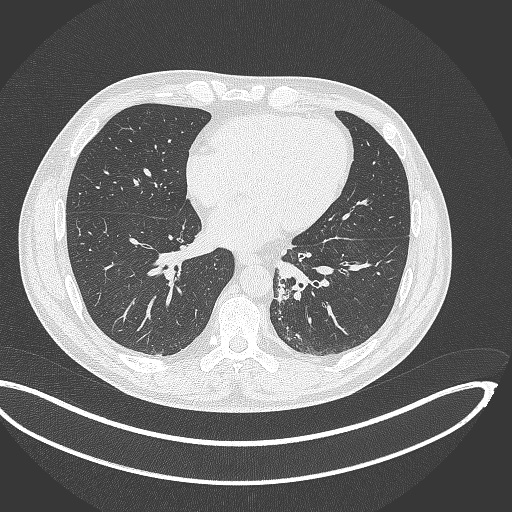
Chest CT, one axial slice; slice 137 of 362 in the series (ordered by position); reconstruction kernel B70f; 120 kVp; lung window (W 1500 / L -600 HU); 512 × 512 image matrix, field of view 442 × 442 mm. Male patient, age 50 years. From the clinical record (not read from this slice): clinical TNM (as recorded): T2a N3 M0.
Annotated regions visible in this slice (bounding box drawn by a radiologist):
- lung tumour (recorded histology: squamous cell carcinoma): bounding box [x1, y1, x2, y2] px = [272, 277, 292, 306]